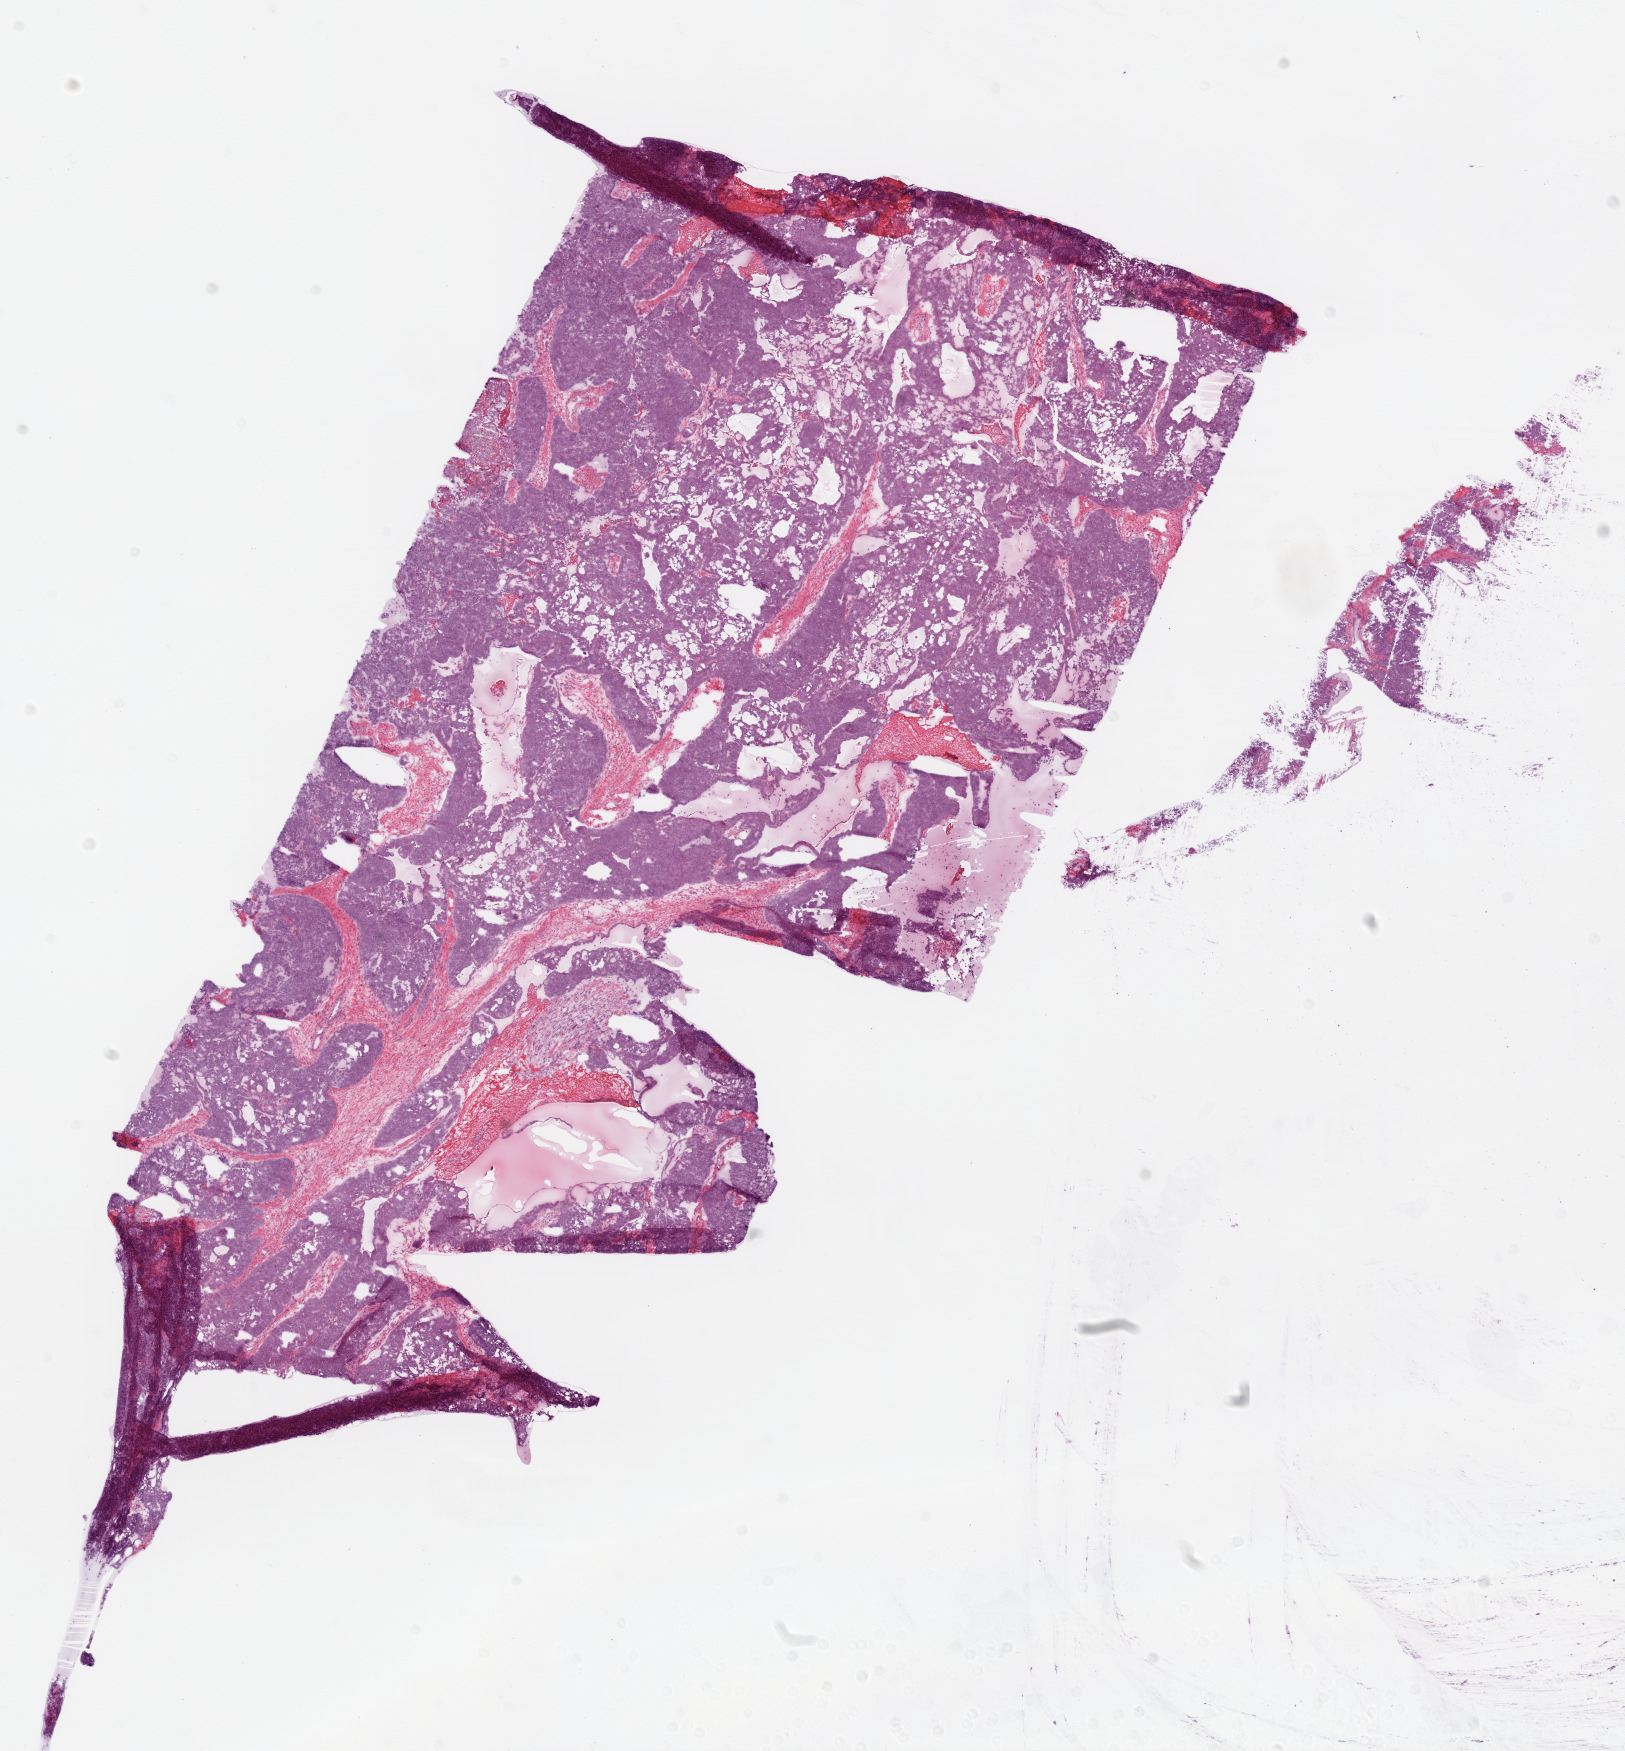
Whole-slide histology image, Hematoxylin and eosin (H&E) stained — whole scanned area (about 13.0 x 14.1 mm) shown as a low-resolution overview, frozen section from the top of the tissue portion, ovary, primary tumour sample. Female, age 83 years at initial diagnosis. Histologic grade: G3 (poorly differentiated). Pathologist review of this section (percent, as recorded): tumour cells 85%, tumour nuclei 95%, normal cells 0%, stromal cells 10%, necrosis 5%.
Pathologic diagnosis: Serous cystadenocarcinoma, NOS. FIGO stage: IIIB.